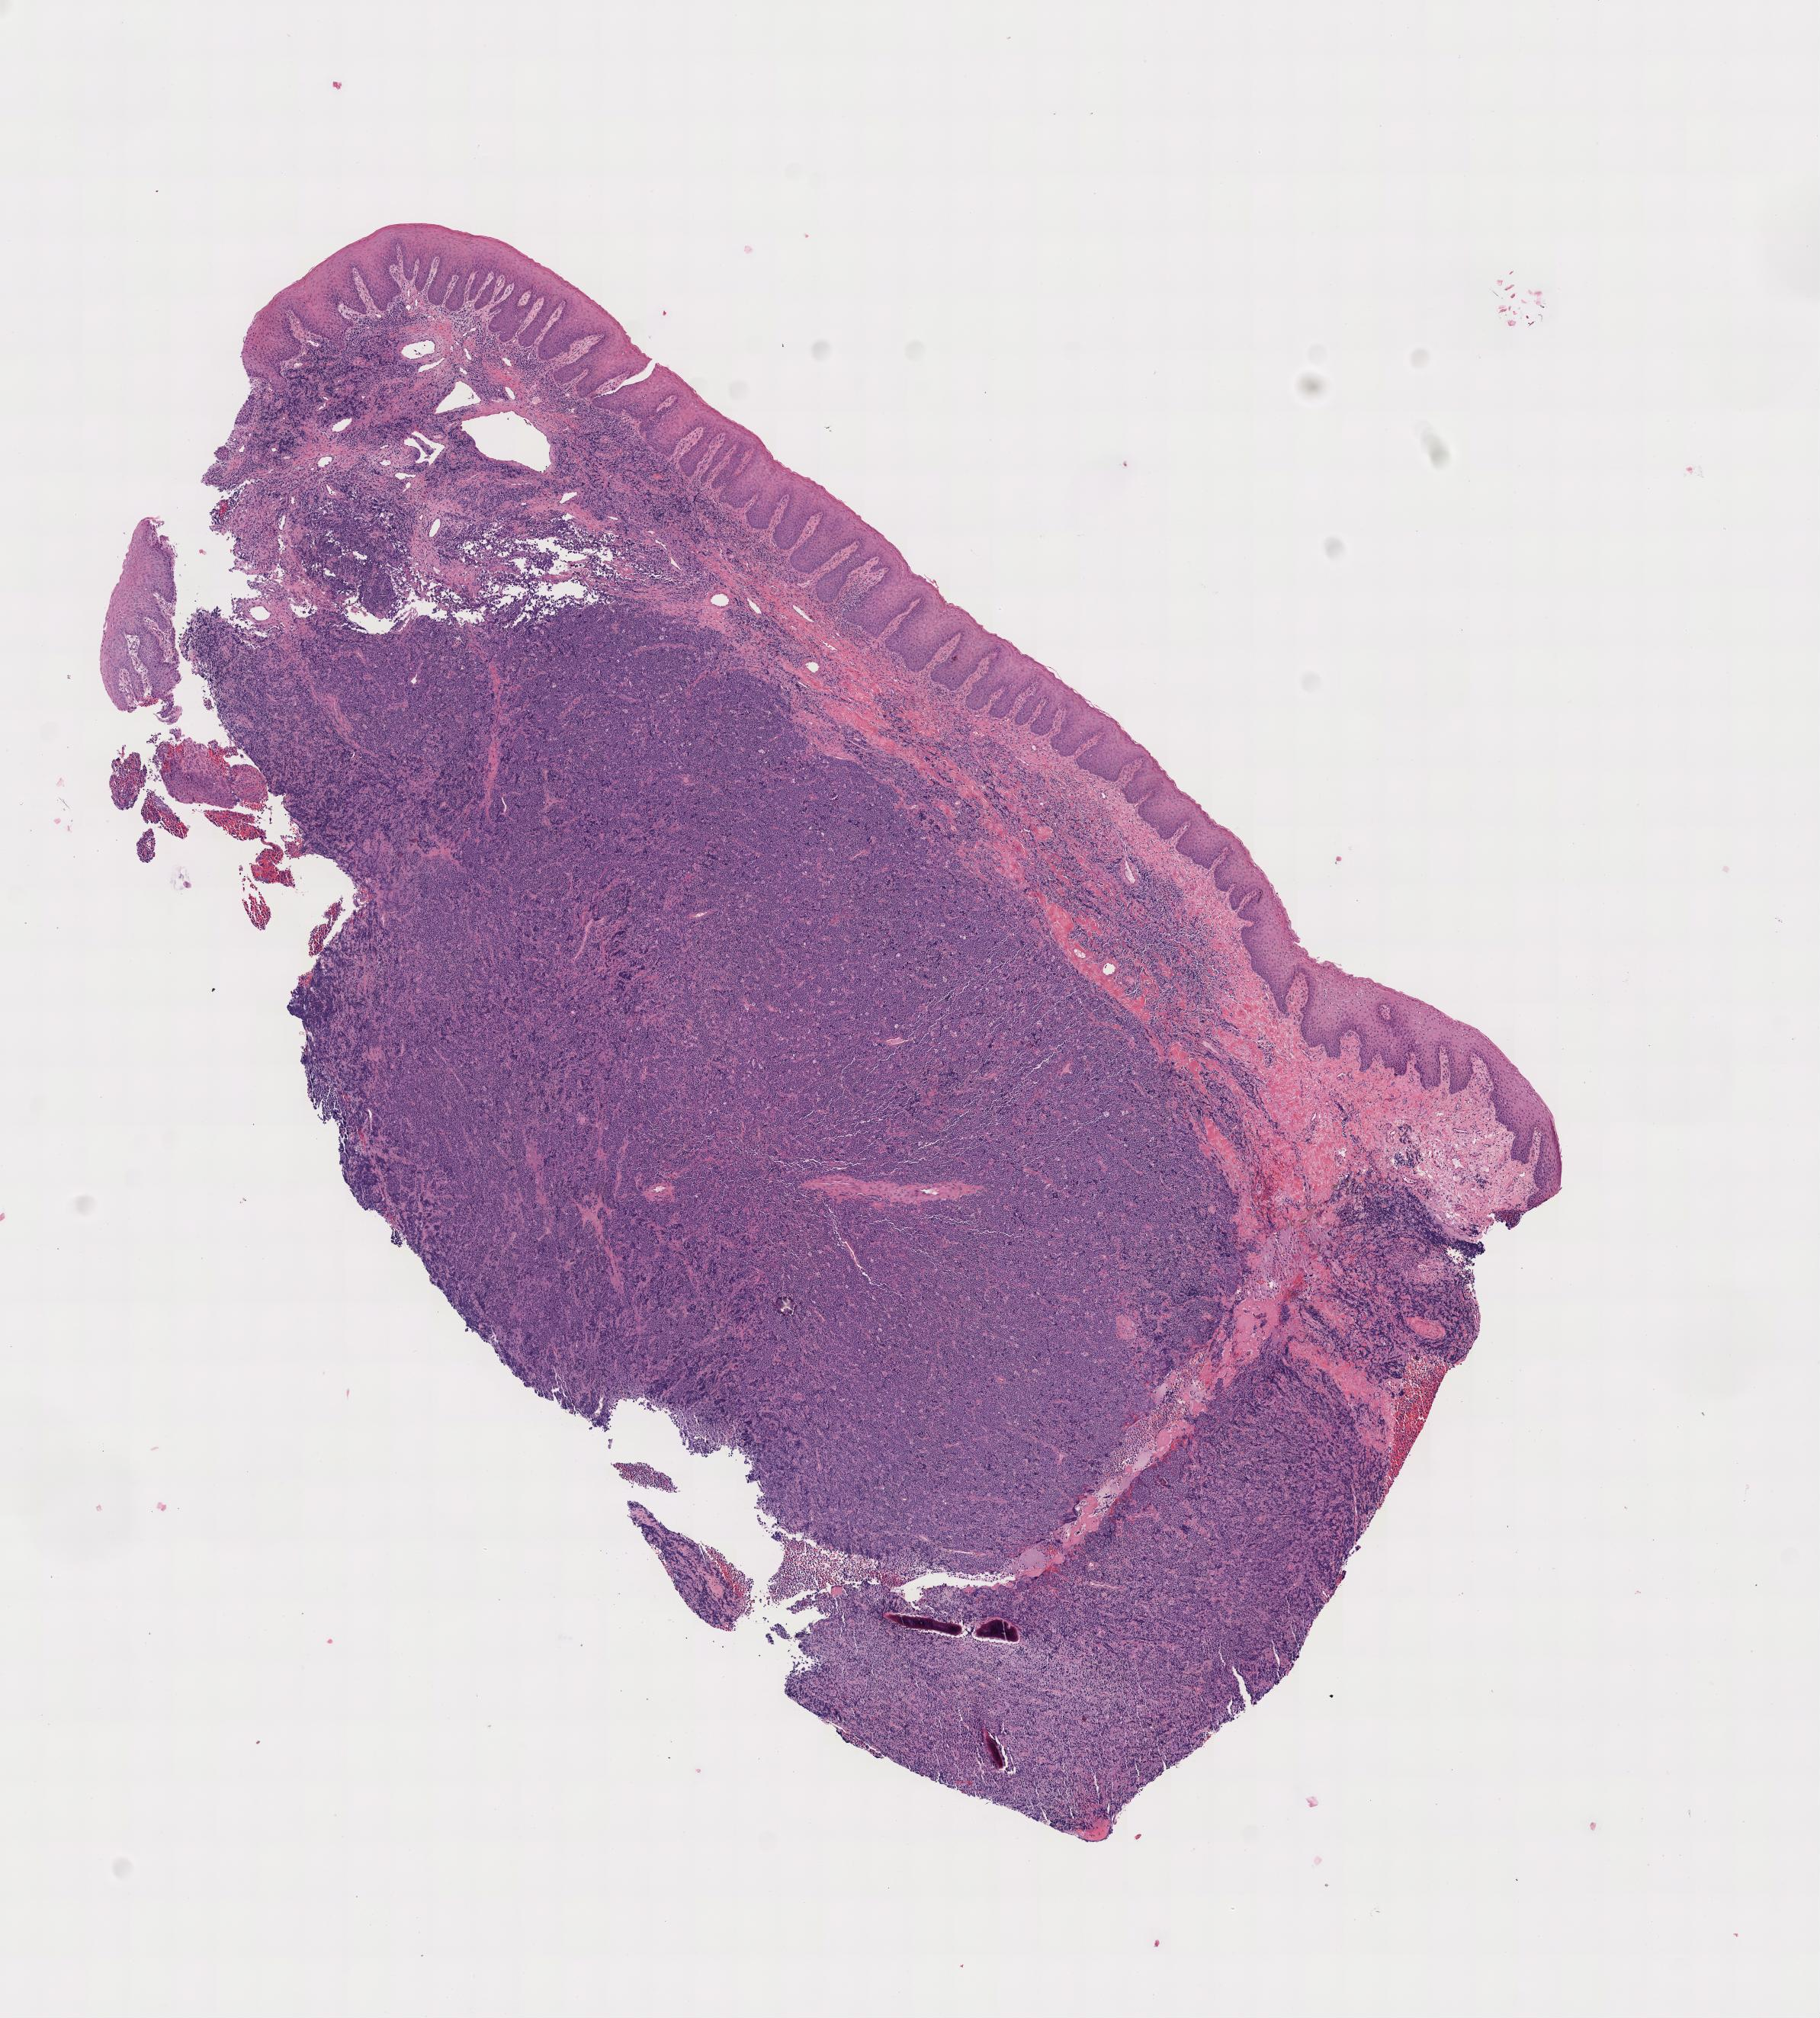
Whole-slide image, hematoxylin and eosin (H&E) stain, whole scanned area shown as a low-resolution overview. Specimen: tumor tissue. Site: cranium. Male, age 6 years at initial diagnosis.
Diagnosis: Burkitt lymphoma, NOS.